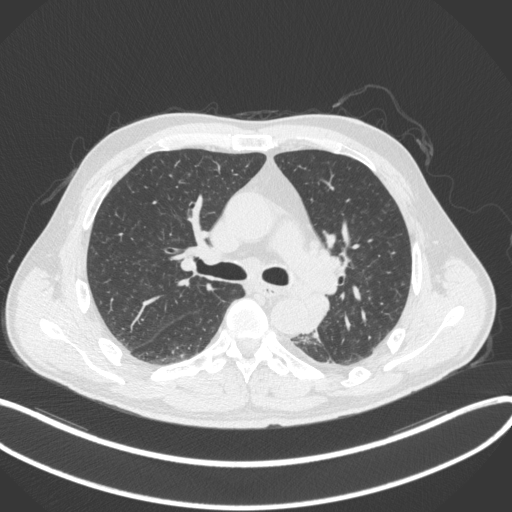
Chest CT, one axial slice. Position 216 of 328 along the scan axis. Reconstruction kernel B31f. 120 kVp. Lung window (W 1500 / L -600 HU). 1 mm slice thickness. 512 × 512 image matrix, field of view 400 × 400 mm. Patient: male, 59 years. Case-level facts recorded for this patient, not image findings: clinical TNM (as recorded): T2a N2 M0.
Annotated regions visible in this slice (rectangle marked by the reading radiologist):
- lung tumour (recorded histology: squamous cell carcinoma): bounding box (x1, y1, x2, y2) in pixels: (302, 289, 333, 332)